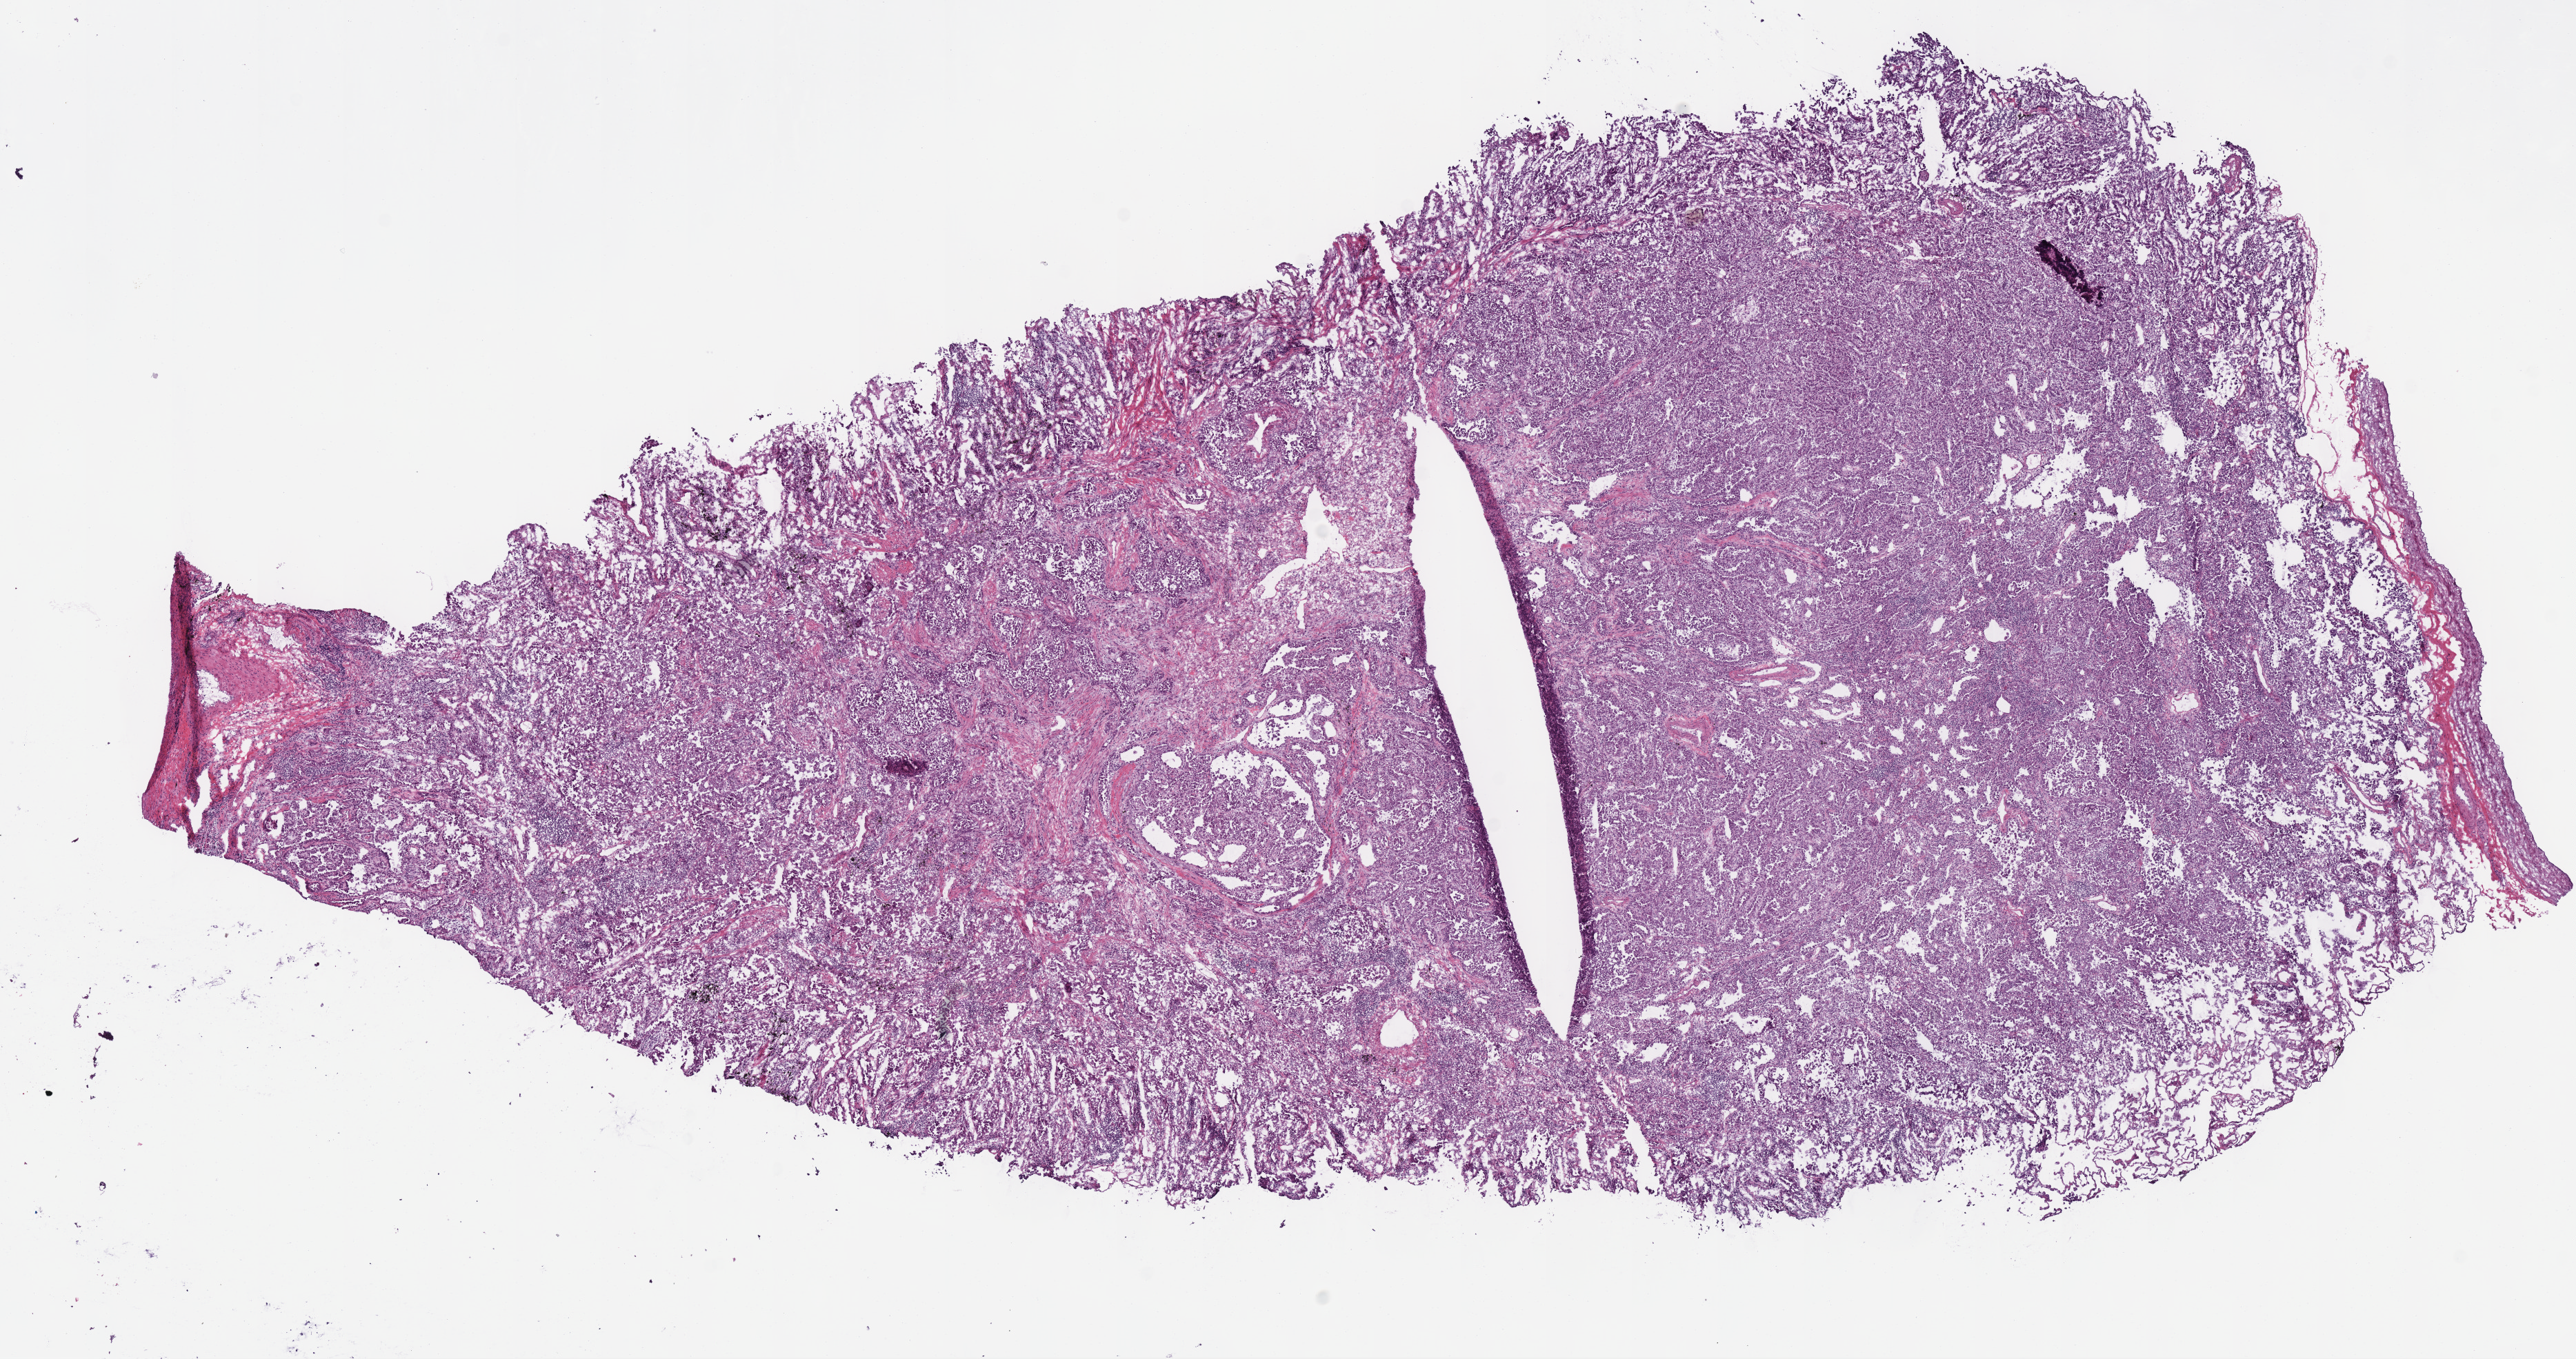
Whole-slide histology image, H&E-stained — a low-resolution overview of the entire scanned area, about 14.7 x 7.7 mm (acquisition: 40x scan). Frozen section from the bottom of the tissue portion. Sample: primary tumour, lung. Male patient; age at initial diagnosis 75 years. Composition of this section per pathologist review: tumour cells 85%, tumour nuclei 85%, normal cells 5%, stromal cells 10%, necrosis 0%.
AJCC pathologic stage: IA. Diagnosis: Adenocarcinoma, NOS (lower lobe, lung).